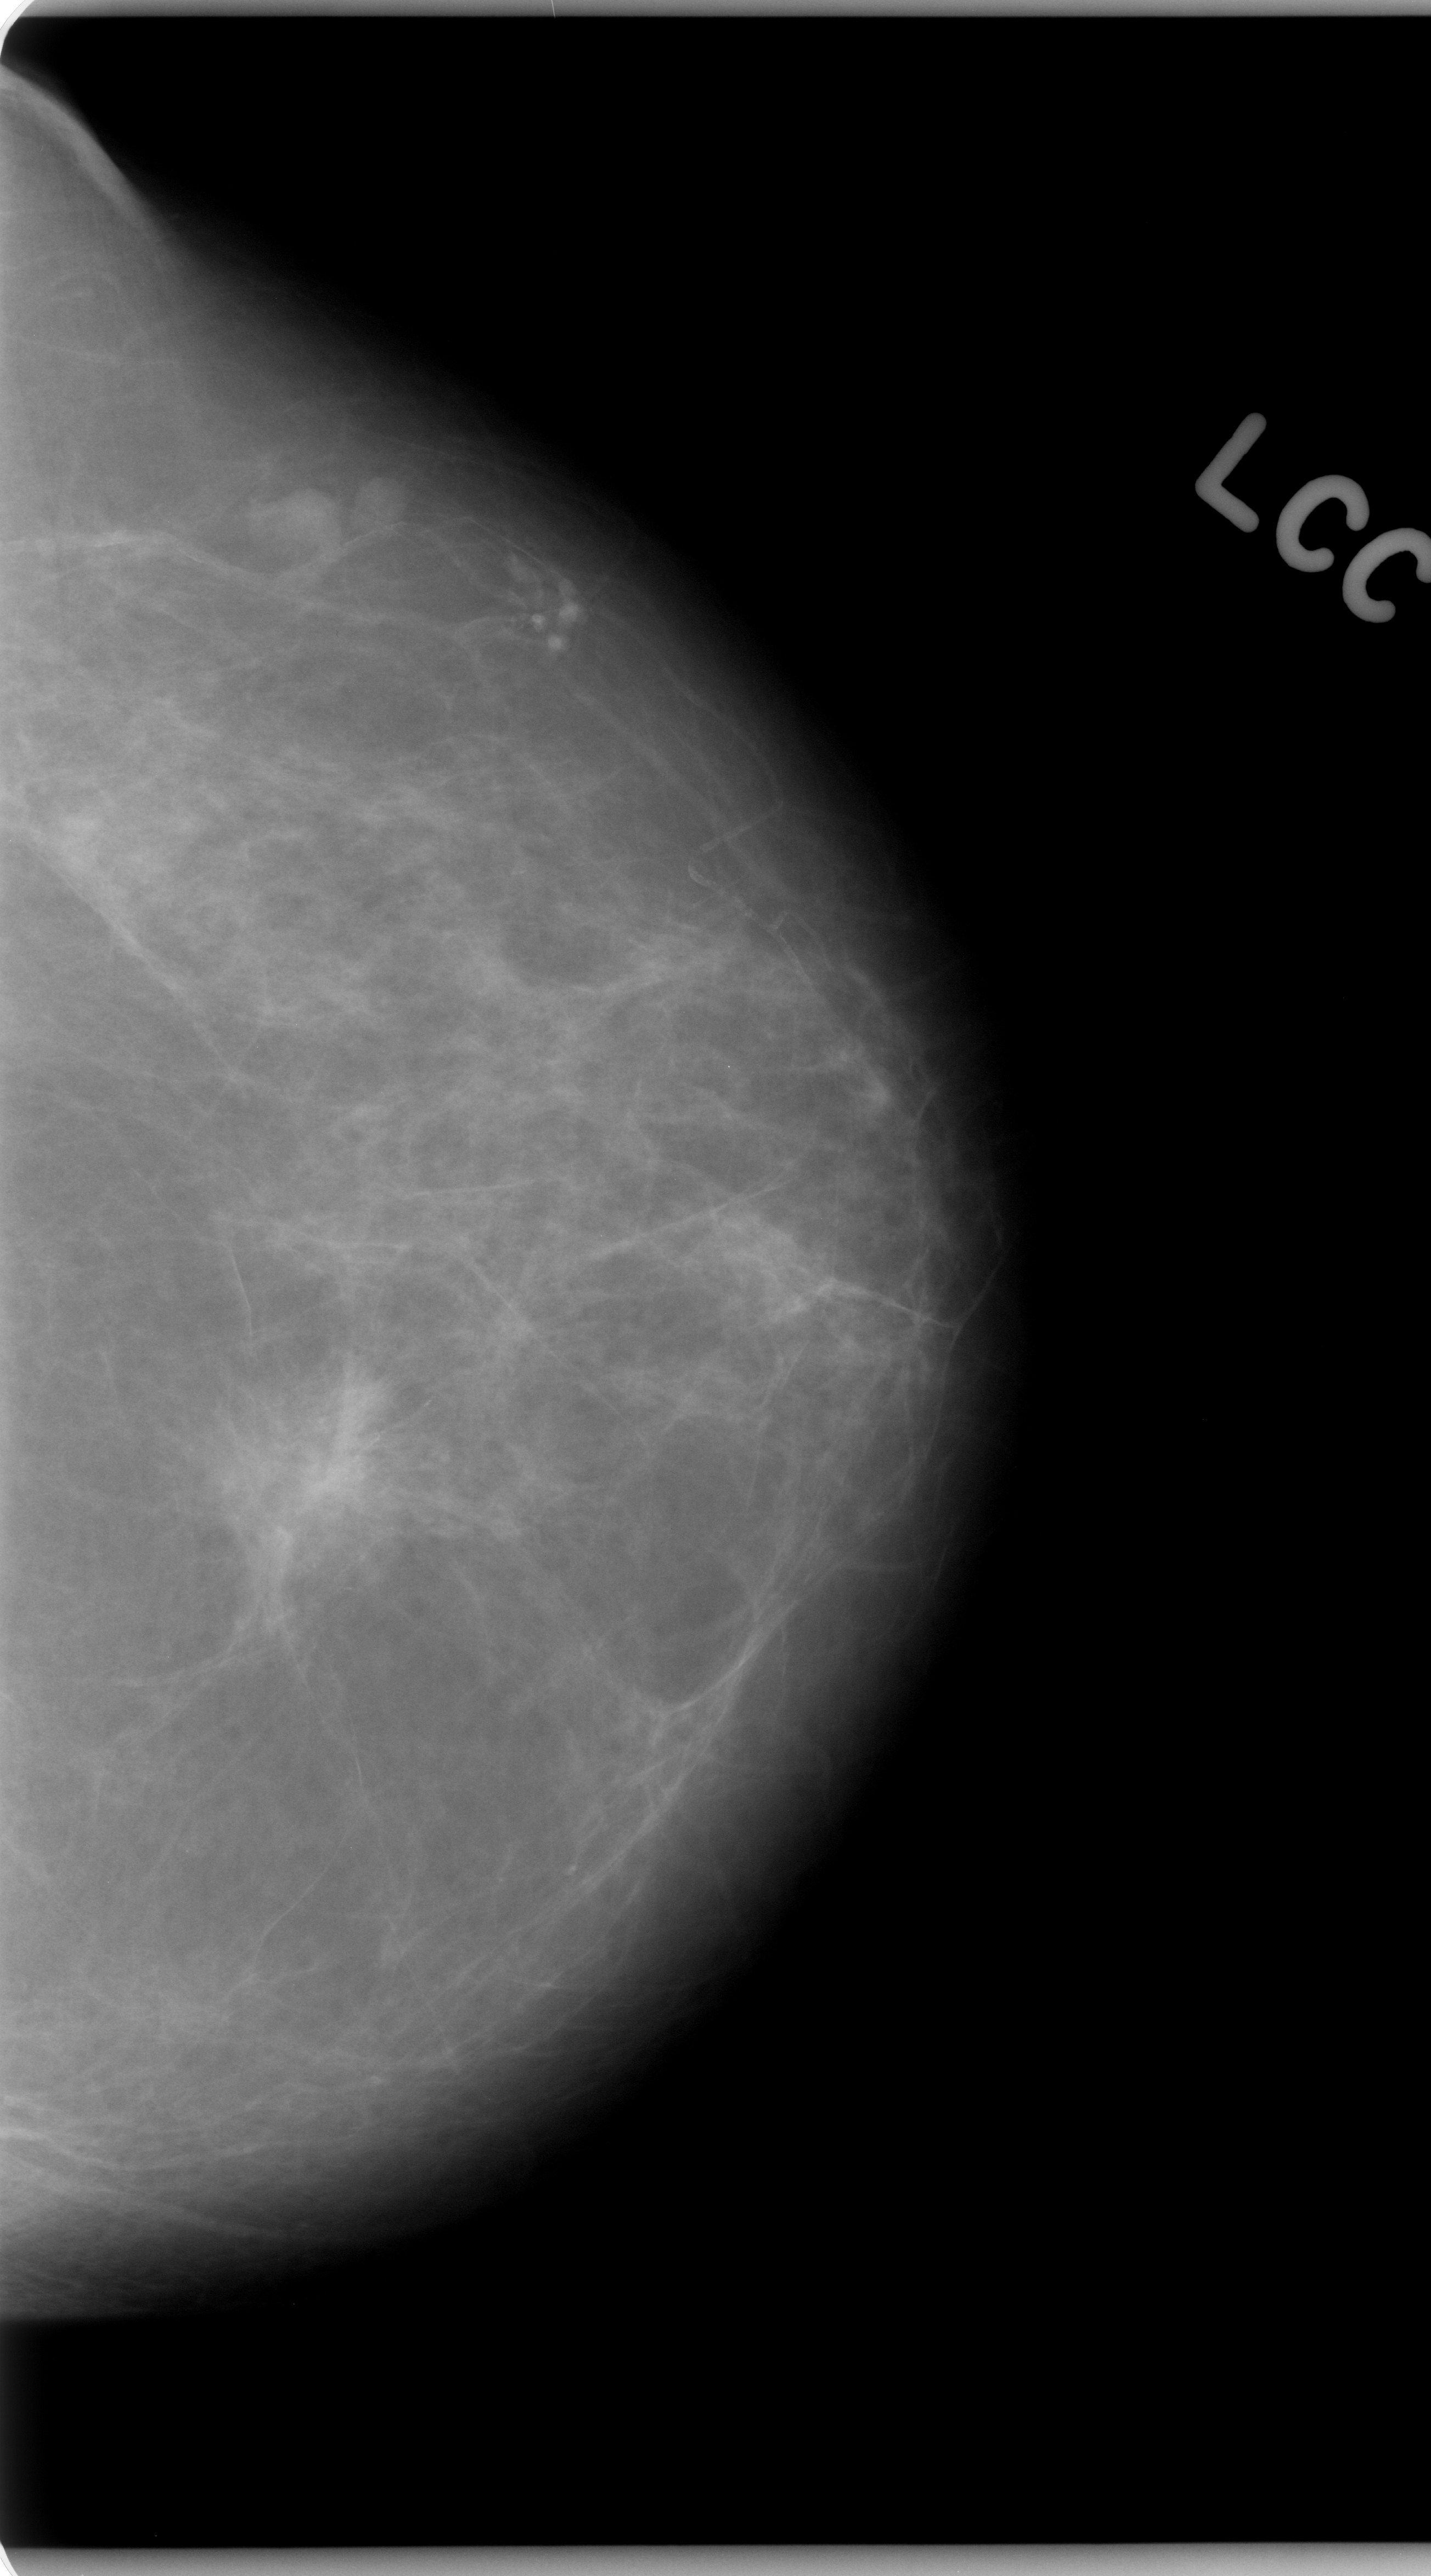
Scanned film-screen mammogram; left breast; craniocaudal (CC) view; BI-RADS breast density category 1 (scale 1–4).
- Calcifications, morphology amorphous, distribution clustered; BI-RADS assessment category 5; pathology (as recorded): malignant.